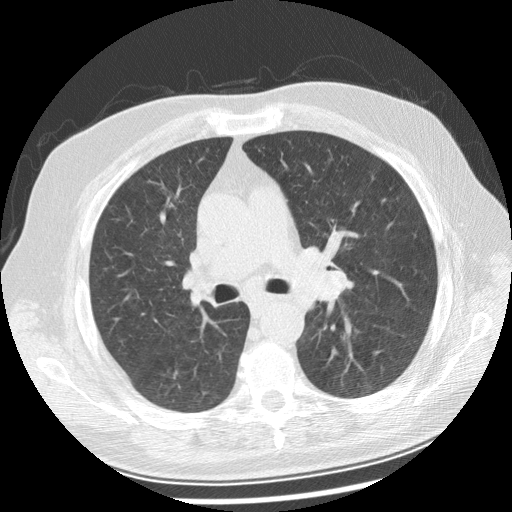
Low-dose screening chest CT, one axial slice; slice 152 of 250 in the series (ordered by position); reconstruction kernel STANDARD; 120 kVp; lung window (W 1500 / L -600 HU); 512 × 512 image matrix.
Outlined on this slice (expert manual segmentation):
- lesion 1 (tumor, left main bronchus): box from (x=316, y=271) to (x=354, y=302) px